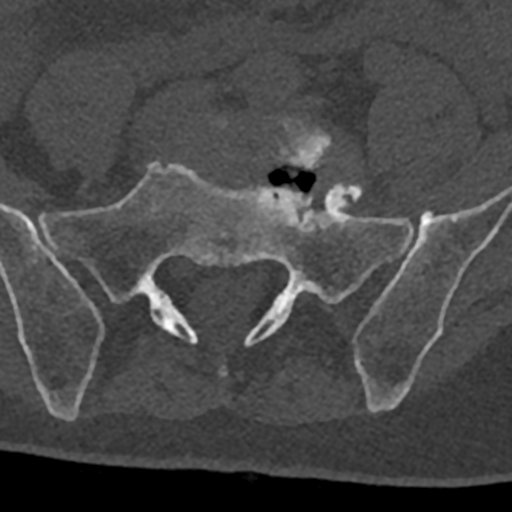
CT including the spine, one axial slice. Position 153 of 797 along the scan axis. Reconstruction kernel Br40s/3. 120 kVp. Bone window (W 1800 / L 400 HU). 0.5 mm slice thickness. 512 × 512 image matrix, field of view 160 × 160 mm. Male patient, age 74 years. Case-level facts recorded for this patient, not image findings: primary cancer: renal.
Structures marked on this image (semi-automatic segmentation, software-assisted and operator-edited):
- L5 vertebra: bounding box (x1, y1, x2, y2) in pixels: (218, 119, 332, 167)